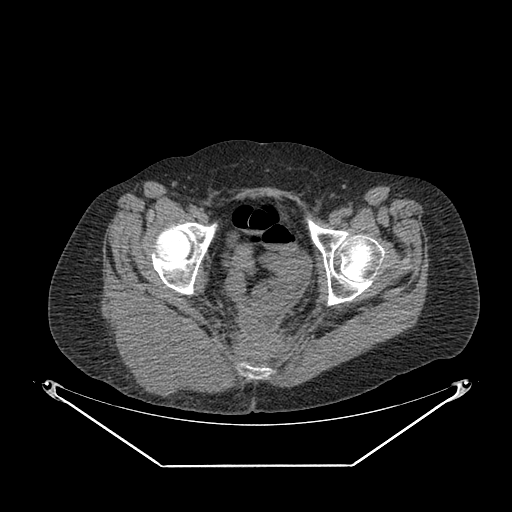
CT of an extremity soft-tissue mass (from a PET/CT study), one axial slice. Reconstruction kernel SOFT. 140 kVp. Soft-tissue window (W 400 / L 40 HU). 3.75 mm slice thickness. 512 × 512 image matrix. Female patient. From the clinical record (not read from this slice): histological type: spindle cell suggestive of myxofibrosarcoma; grade: intermediate; site of the primary tumour: right buttock.
Annotated regions visible in this slice (expert contour drawn on MRI and transferred to this co-registered scan by the dataset authors):
- gross tumour volume (mass): bounding box <109,301,218,400> (left, top, right, bottom; pixels)